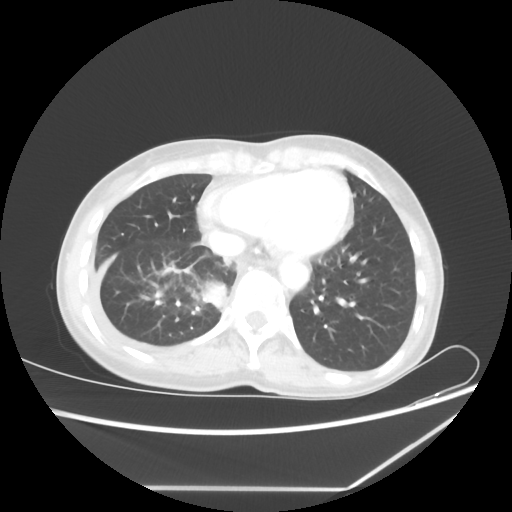
Chest CT, one axial slice. Position 18 of 60 along the scan axis. Reconstruction kernel STANDARD. Lung window (W 1500 / L -600 HU). 5 mm slice thickness. 512 × 512 image matrix, field of view 364 × 364 mm. Female patient, age 59 years. From the clinical record (not read from this slice): clinical TNM (as recorded): T1c N1 M1.
Annotated regions visible in this slice (bounding box drawn by a radiologist):
- lung tumour (recorded histology: adenocarcinoma): bounding box (x1, y1, x2, y2) in pixels: (201, 280, 228, 308)